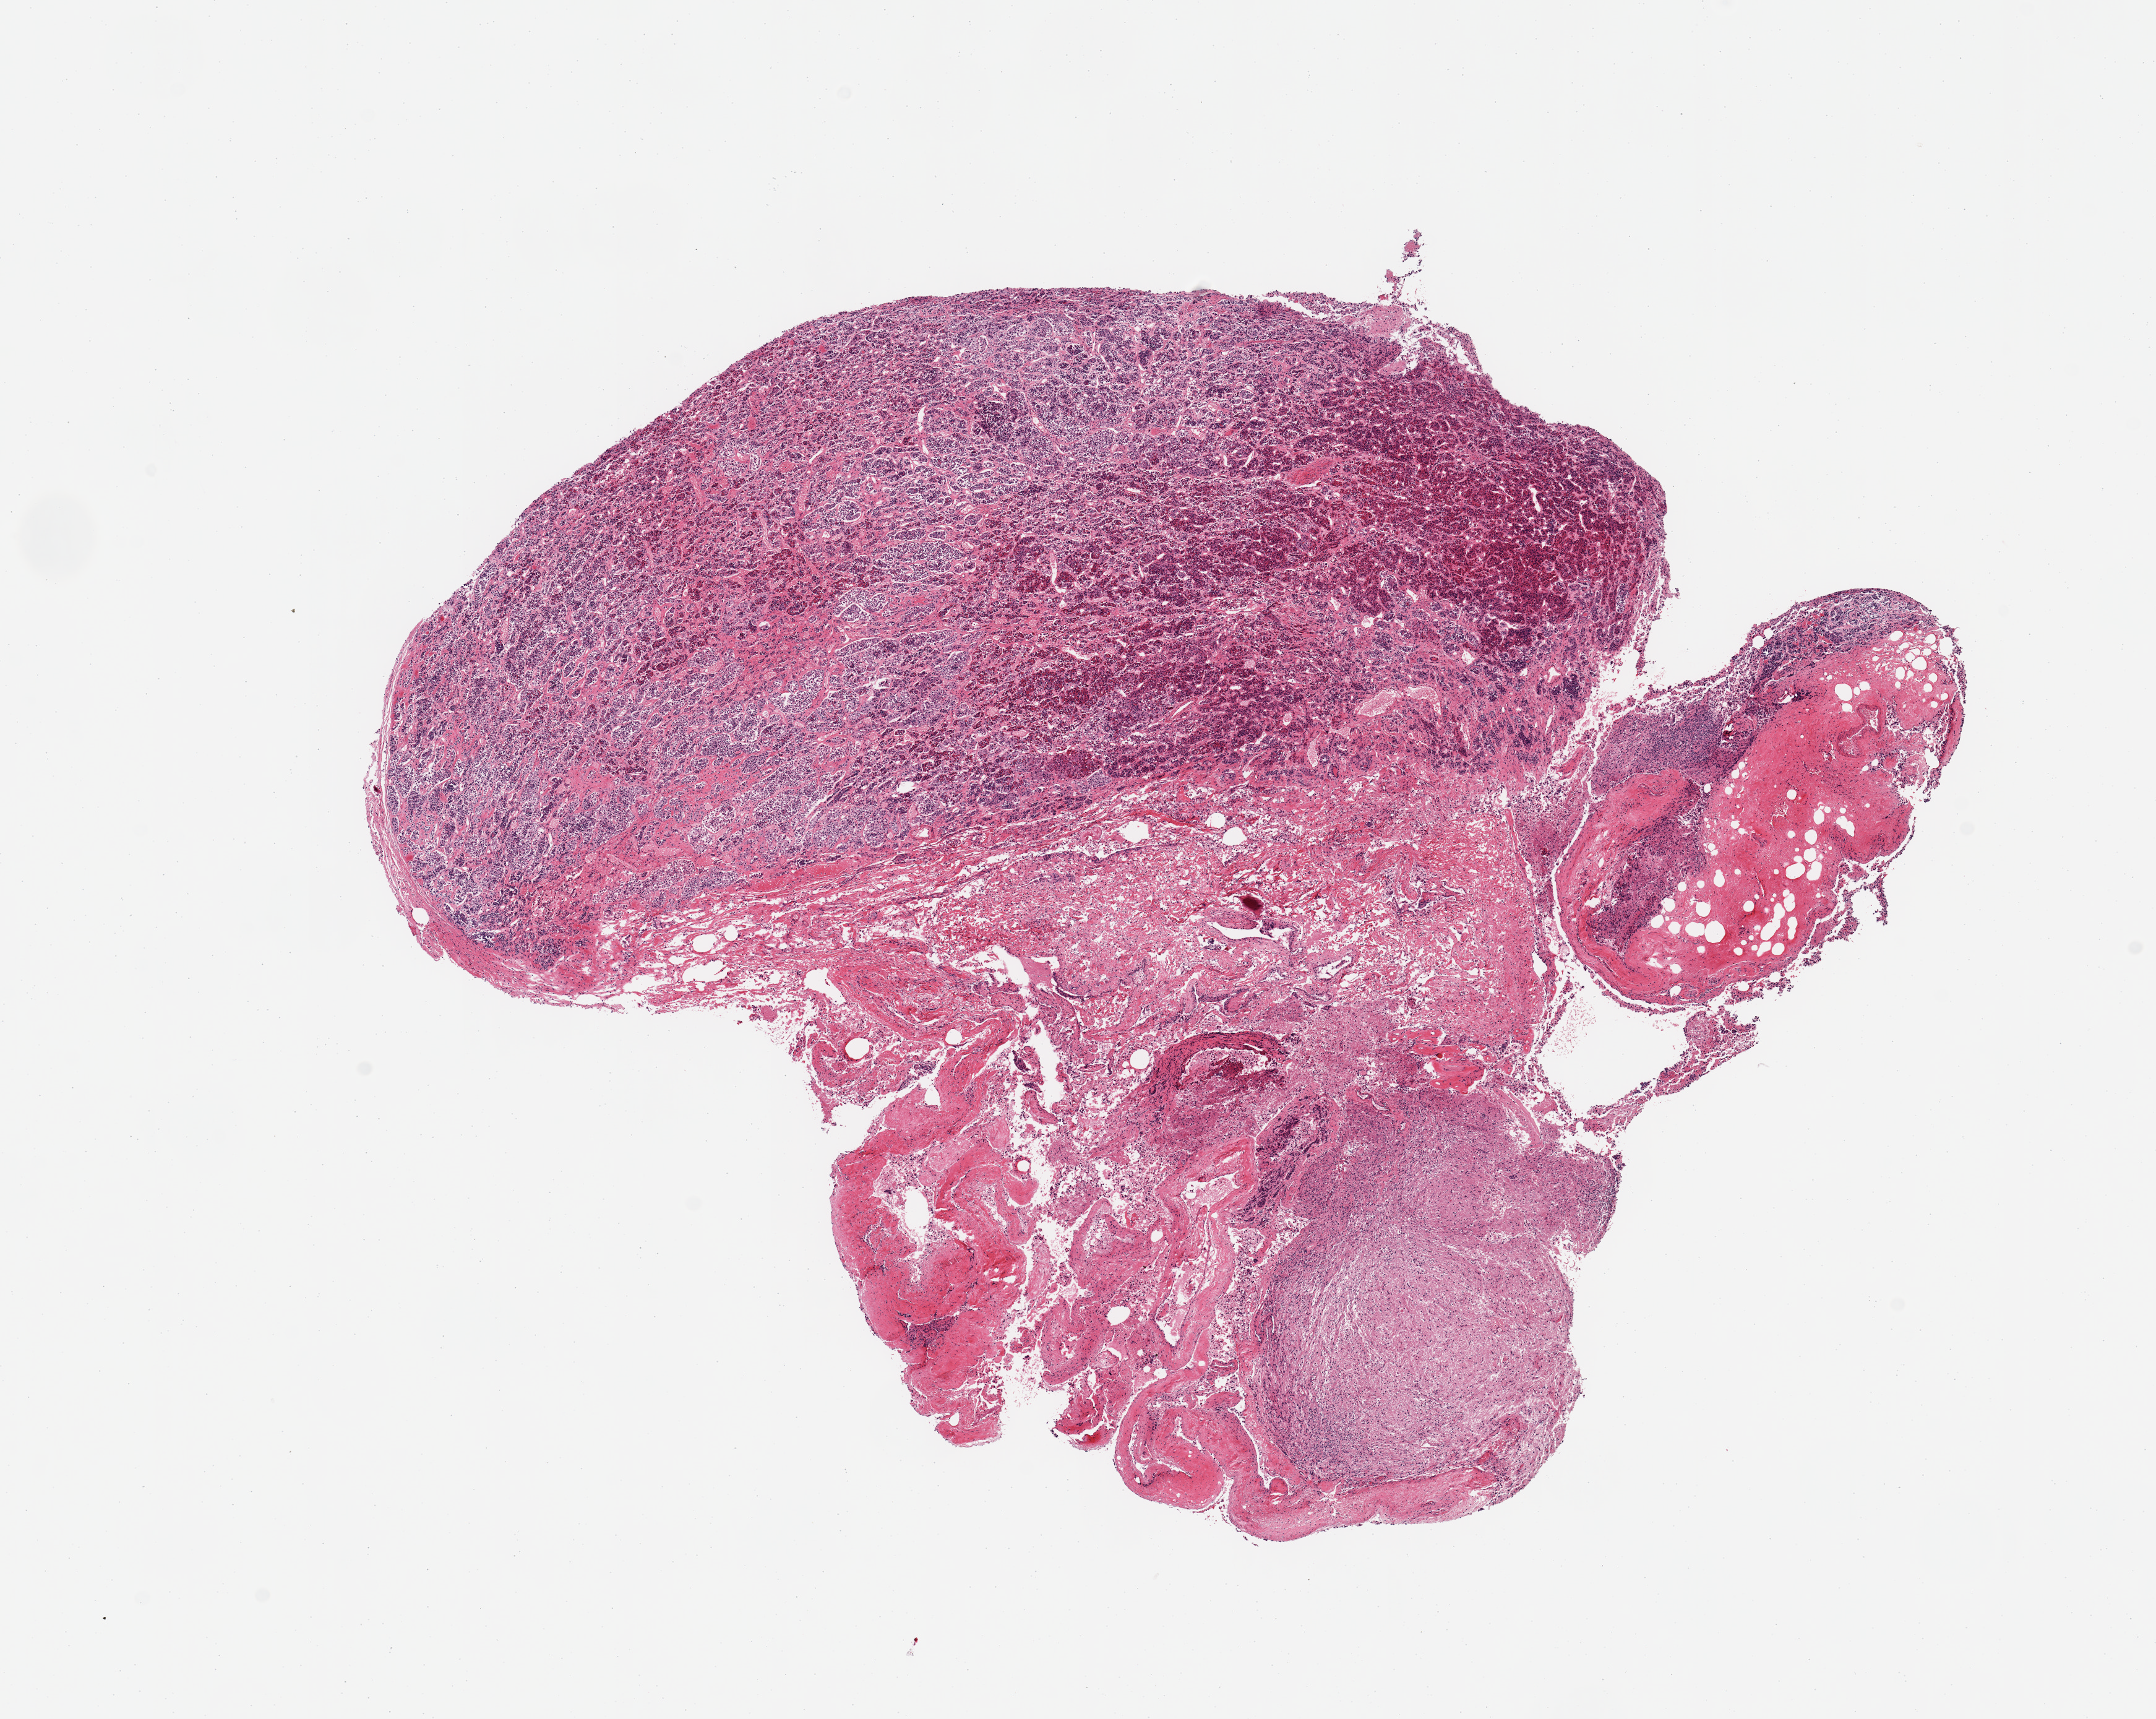
Whole-slide image, hematoxylin and eosin (H&E) stain, brightfield — low-resolution overview of the scanned area, about 13.8 x 11.0 mm; PAXgene-fixed, paraffin-embedded tissue; section of pituitary (target tissue); tissue donor sample. Female donor.
Review note (as recorded): 1 piece; adenohypophysis and neurohypophysis, portion of dura.